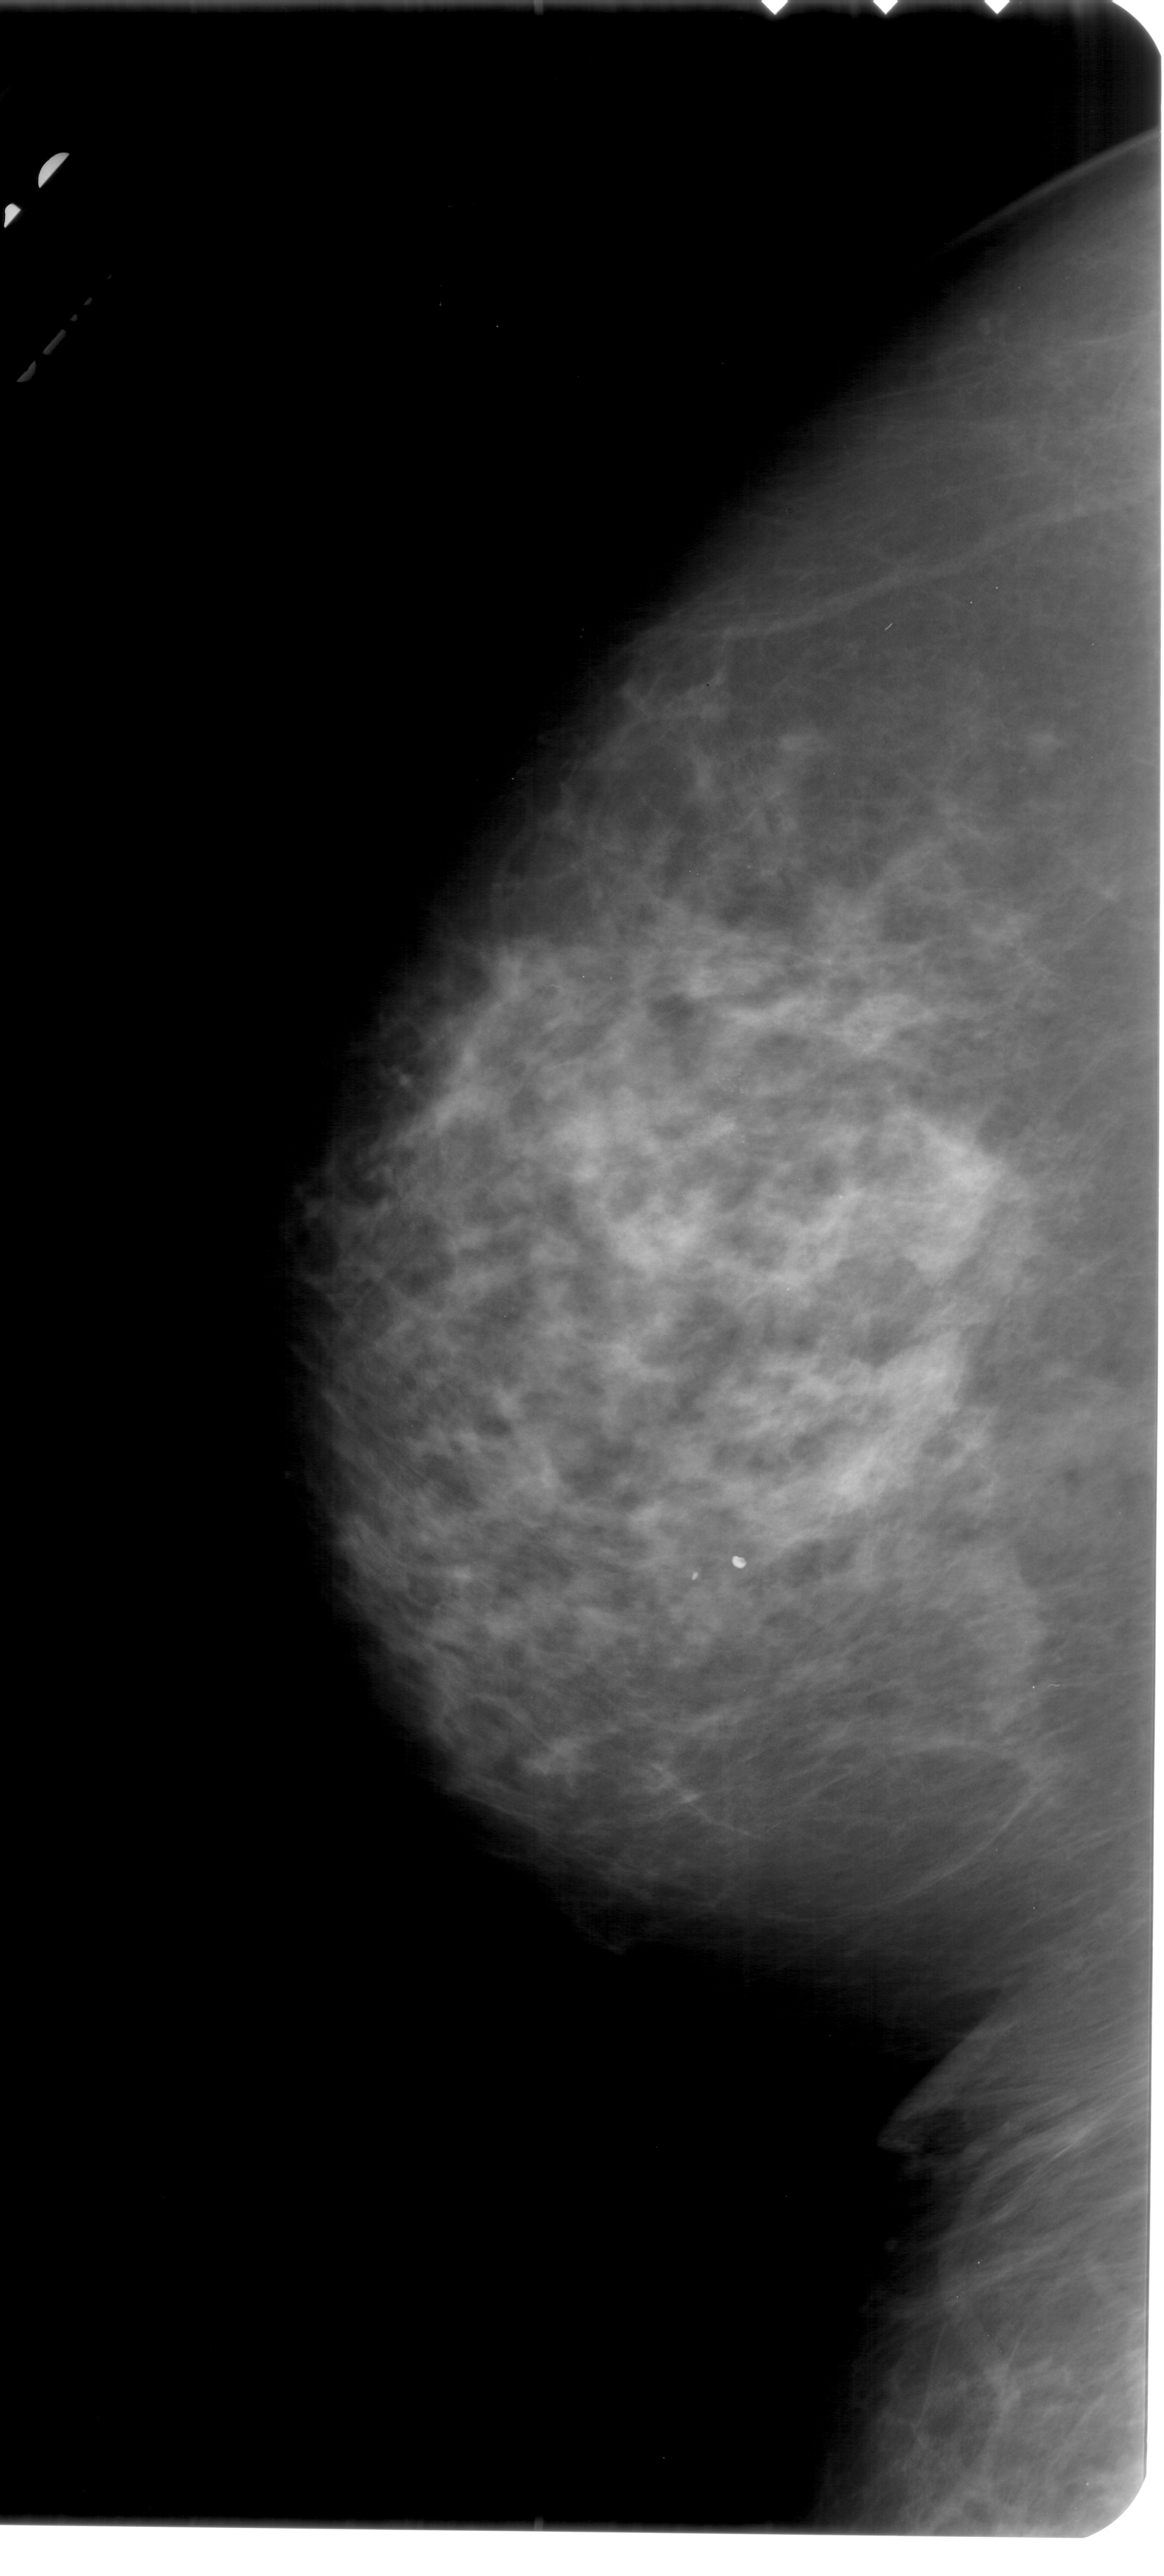
Digitized screen-film mammogram. Left breast. CC view. 1164 × 2576 image matrix.
Expert-marked regions of interest on this image (one box per marked abnormality):
- calcifications, morphology pleomorphic, distribution clustered; BI-RADS assessment category 4; pathology (as recorded): malignant: box from (x=699, y=1054) to (x=770, y=1154) px